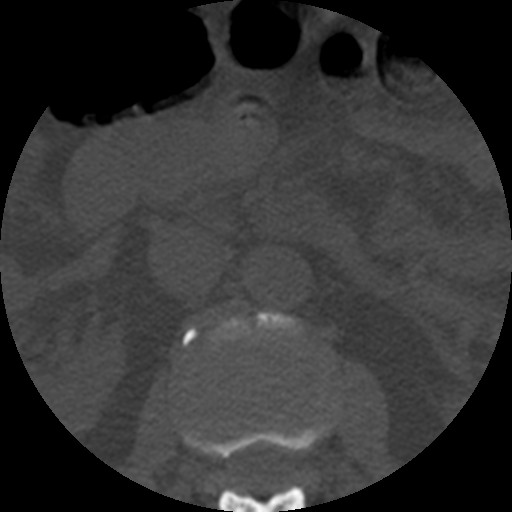
CT including the spine, one axial slice; slice 171 of 508 in the series (ordered by position); reconstruction kernel STANDARD; bone window (W 1800 / L 400 HU); 1.25 mm slice thickness; 512 × 512 image matrix. Patient age 57 years. Case-level facts recorded for this patient, not image findings: primary cancer: prostate.
Annotated regions visible in this slice (semi-automatic segmentation, software-assisted and operator-edited):
- L1 vertebra: box from (x=182, y=423) to (x=332, y=512) px
- L2 vertebra: (x=183, y=313)–(x=300, y=492)